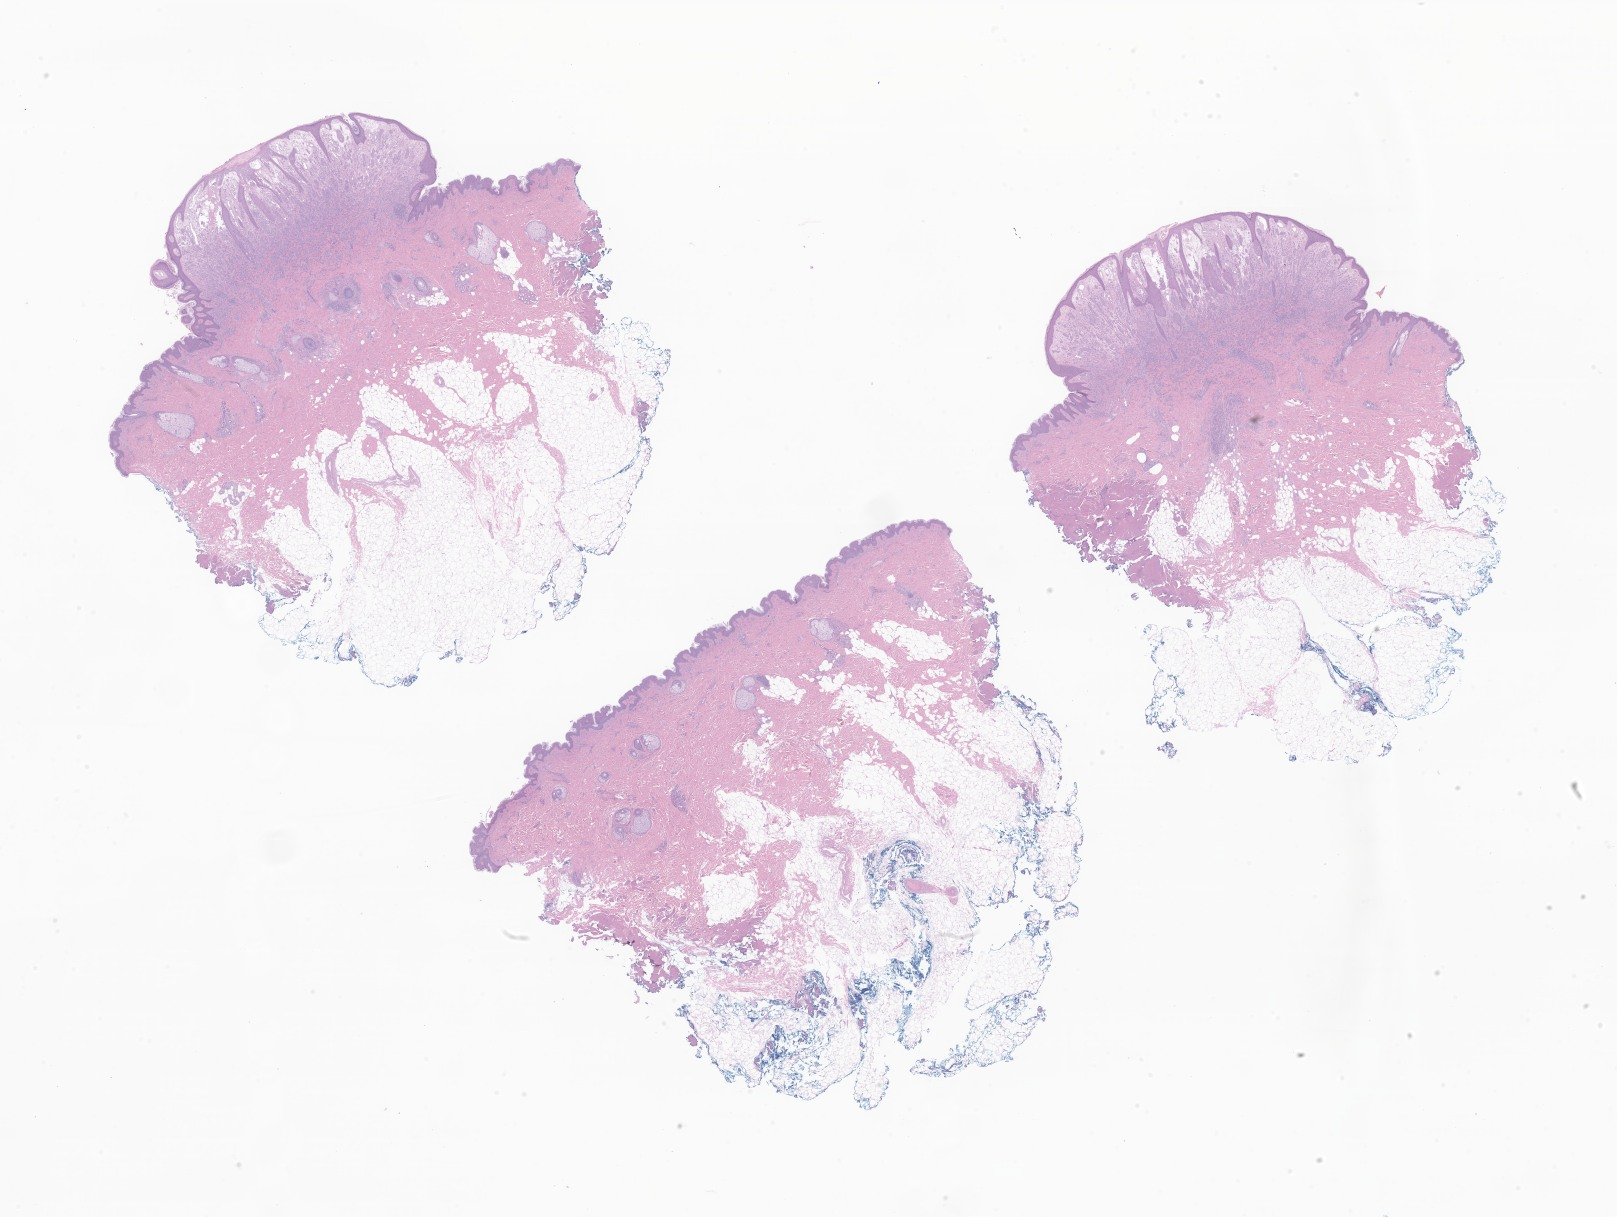
Whole-slide image, H&E stain of tumor tissue from the skin of trunk, a low-resolution overview of the entire scanned area, about 27.3 x 20.5 mm, FFPE section. Patient: male, age 133 months (11 years 1 month).
Diagnosis: Nodular melanoma.